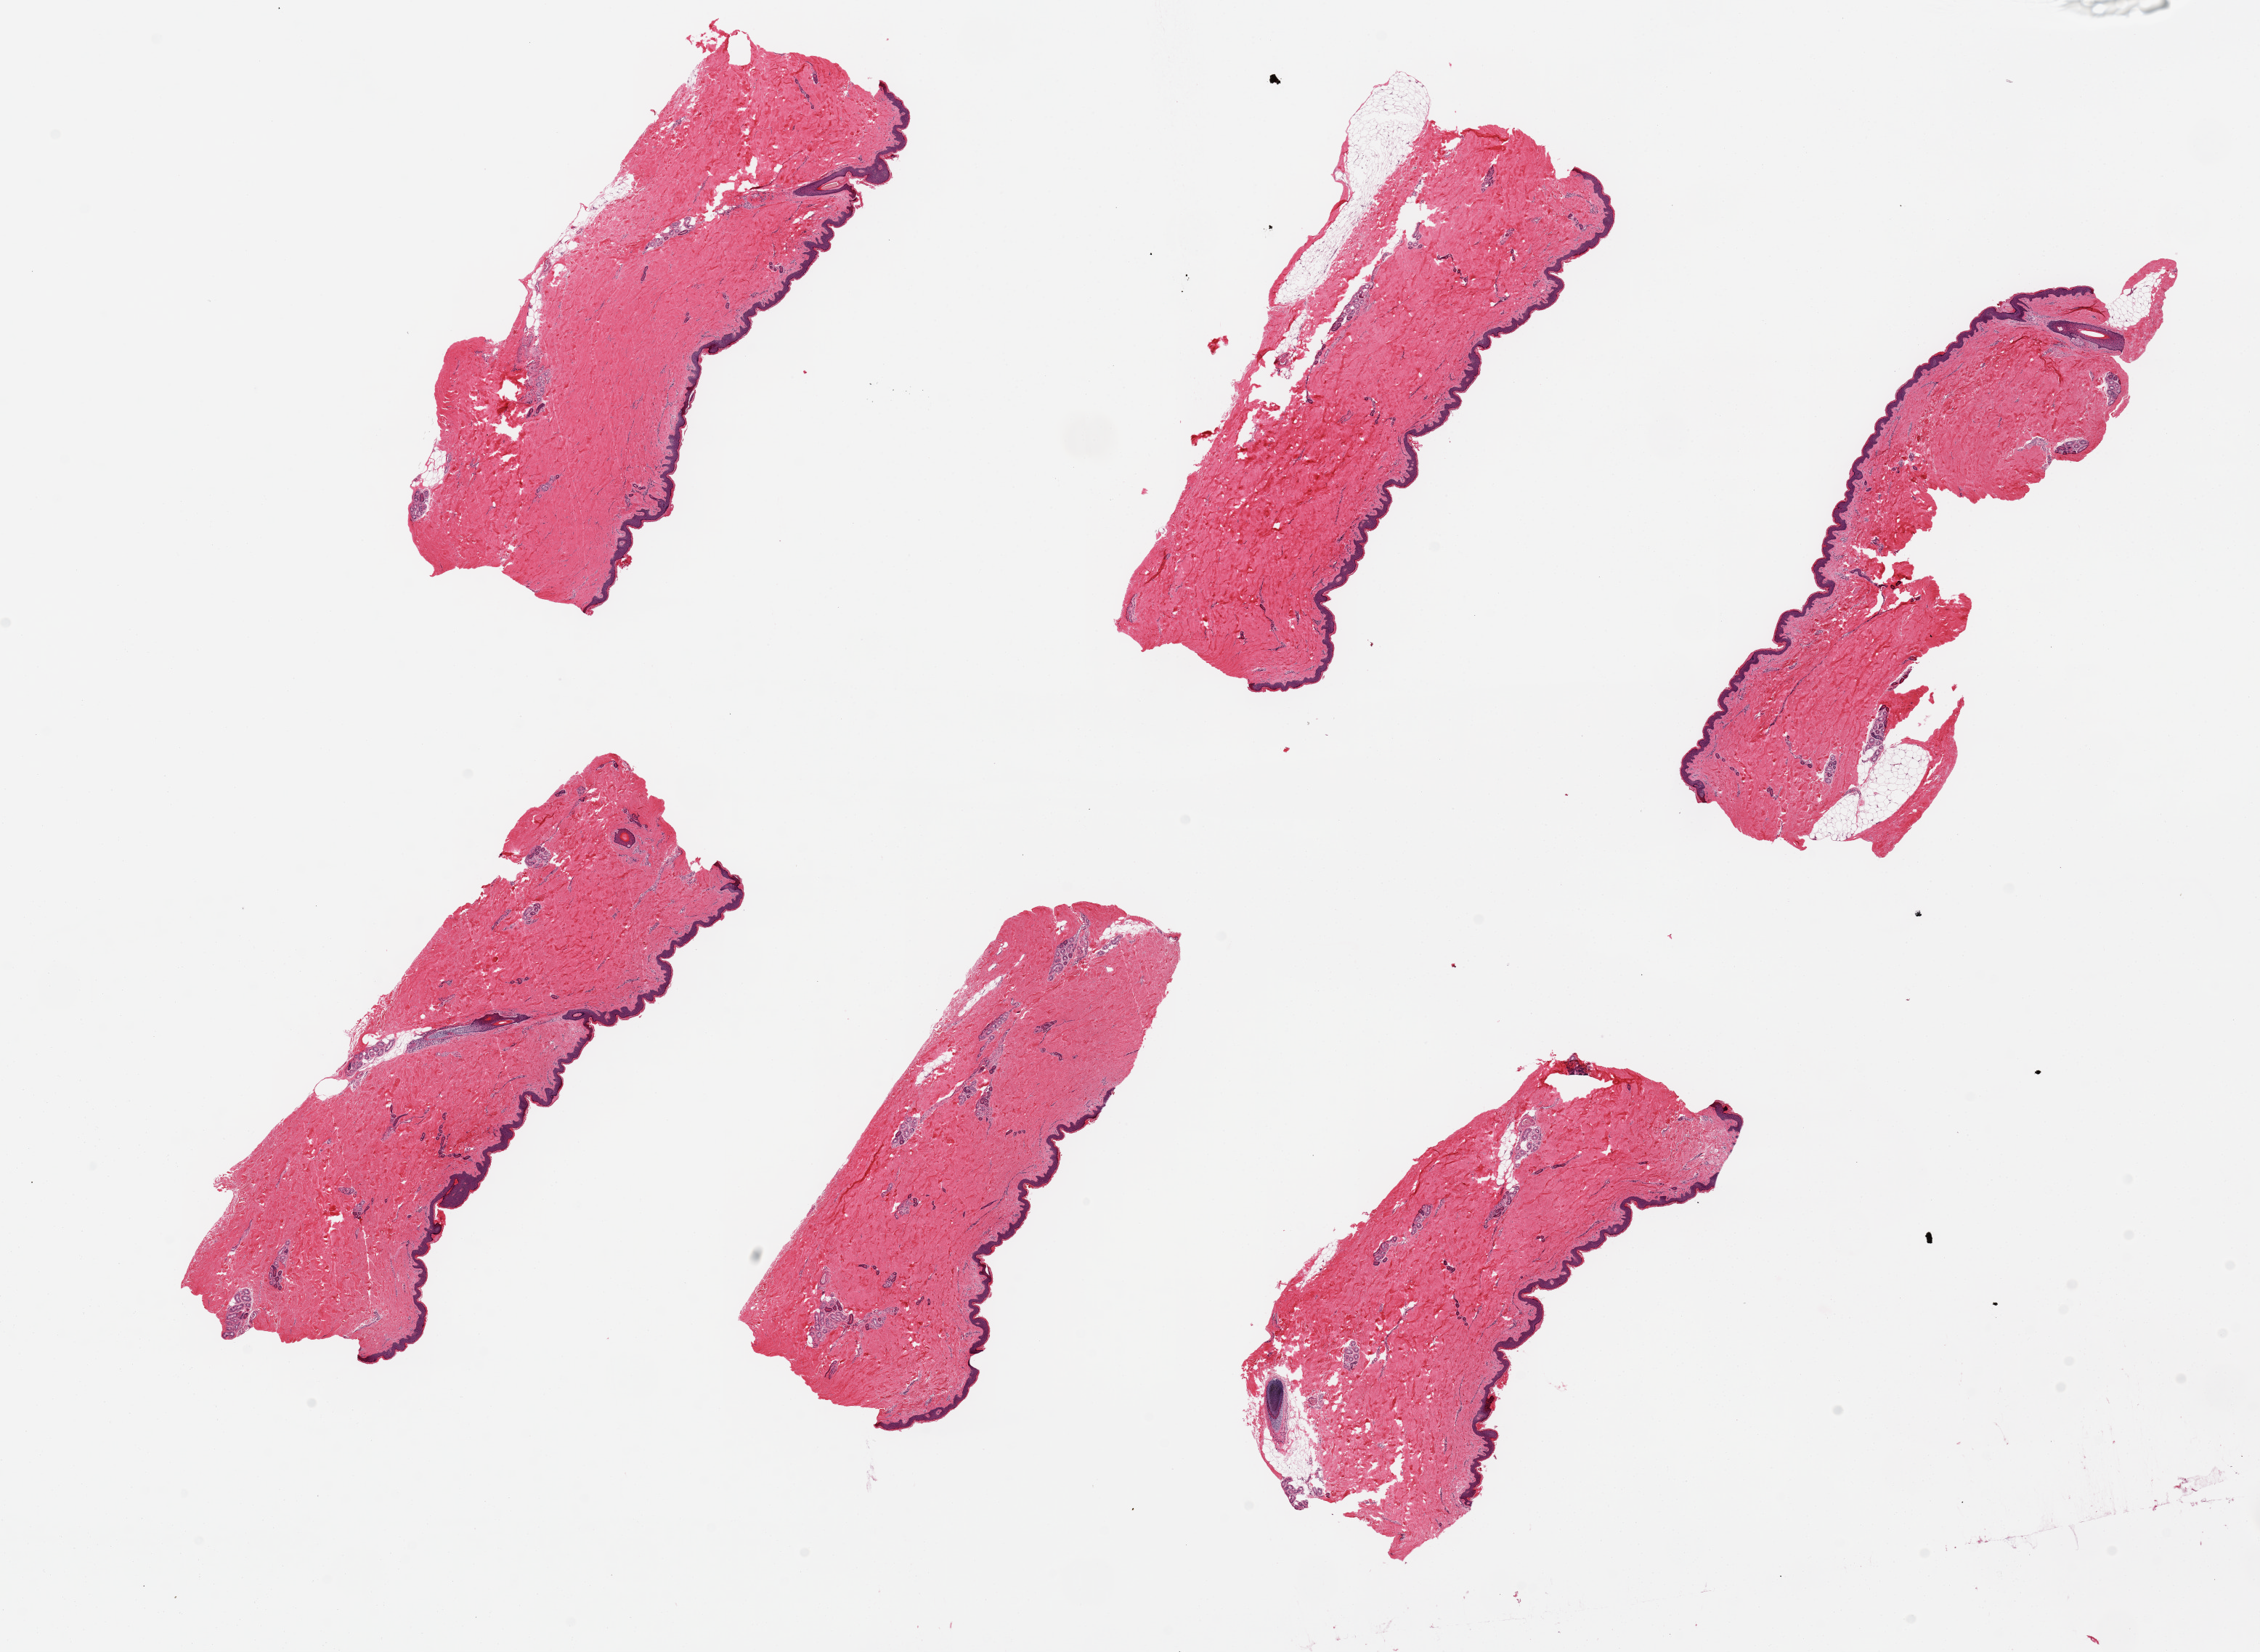
Whole-slide image, H&E stain, brightfield — whole scanned area (about 24.6 x 18.0 mm, from a 20x scan) shown as a low-resolution overview, PAXgene-fixed, paraffin-embedded tissue, section of skin of suprapubic region (target tissue), donor tissue sample. Donor sex: male.
Pathologist's review note for this sample: 6 pieces. up to 7.5x3mm; squamous epithelium is ~4-5% thickness.